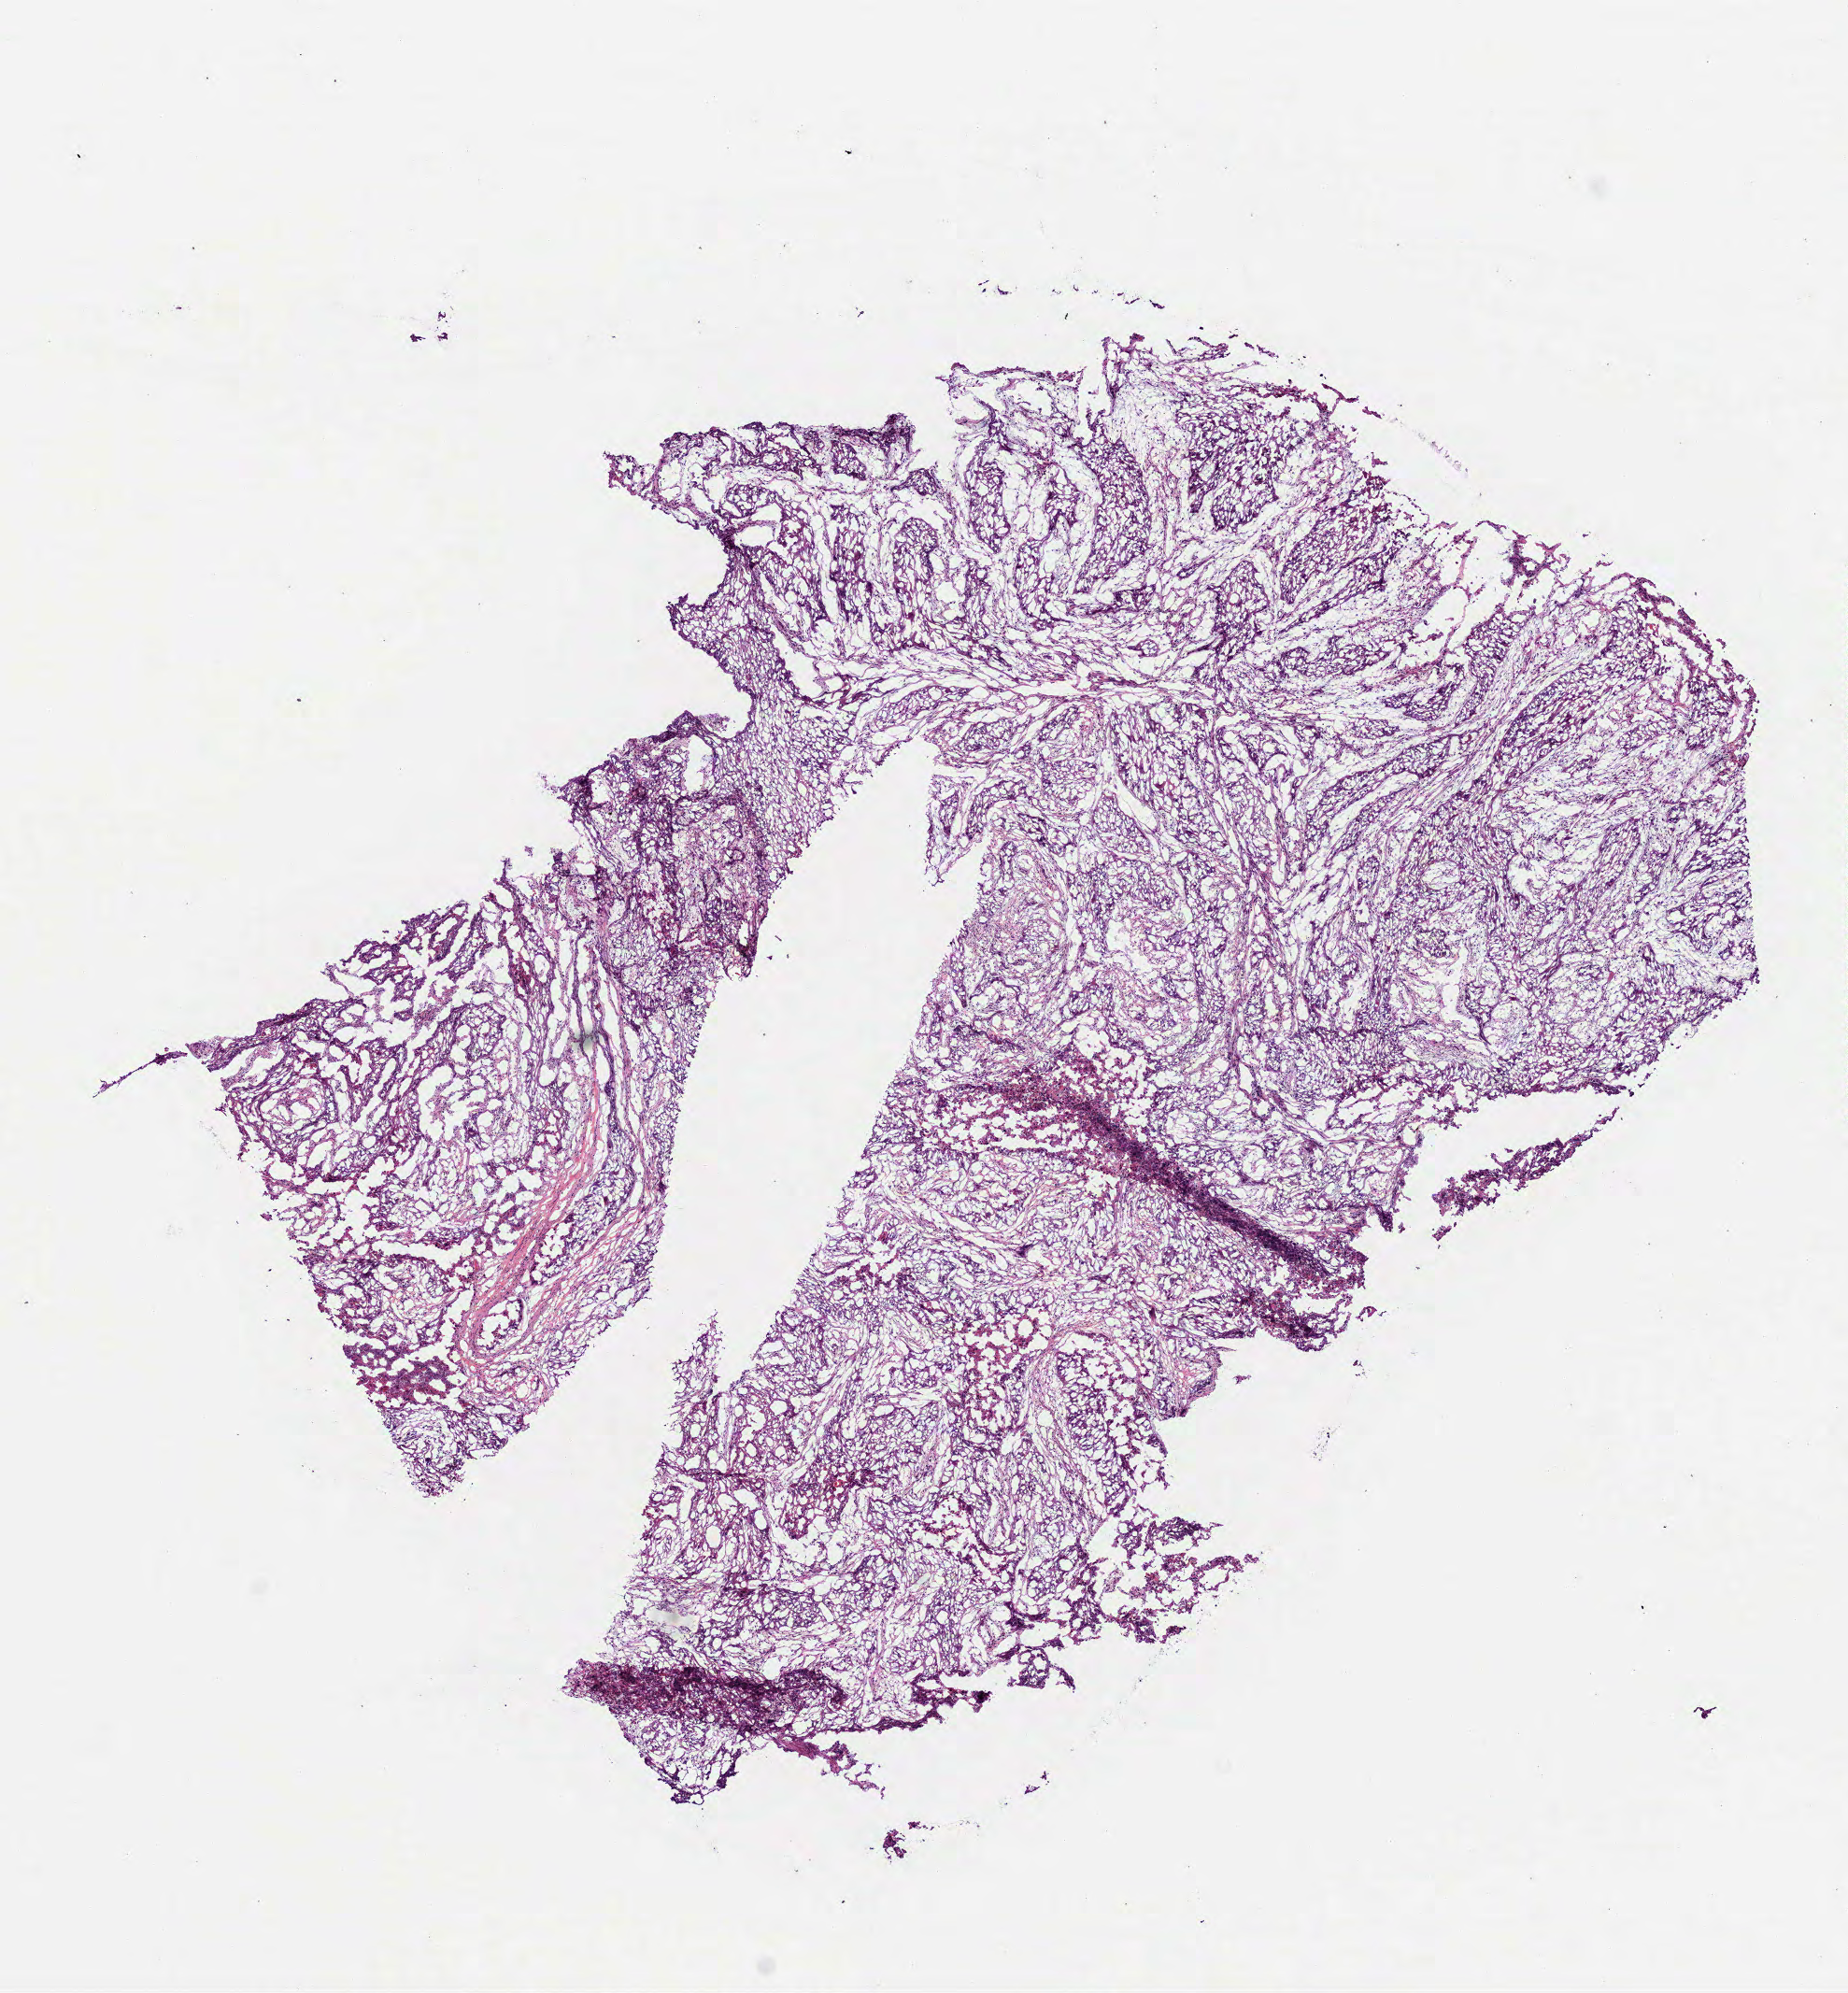
Hematoxylin and eosin (H&E) stained whole-slide image, a low-resolution overview of the entire scanned area, about 8.0 x 8.6 mm (slide scanned at 40x); frozen section; primary tumour sample from the lung. Patient: female, age at initial diagnosis 60 years. Slide review estimates, as recorded: tumour cells 98%, tumour nuclei 61%.
Diagnosis: Squamous cell carcinoma, NOS.